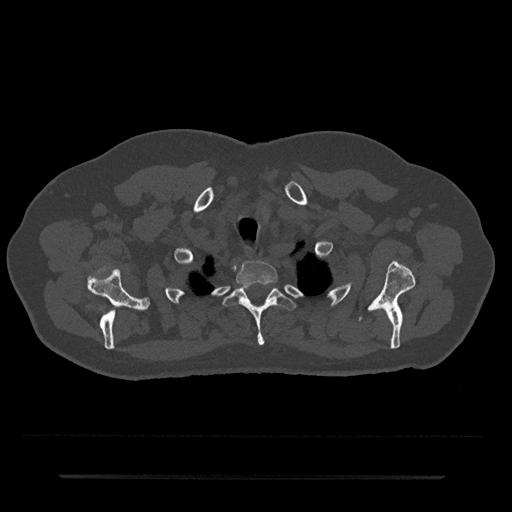
CT including the spine, one axial slice. Position 616 of 797 along the scan axis. Bone window (W 1800 / L 400 HU). 512 × 512 image matrix, field of view 437 × 437 mm. Patient: male, 69 years. Case-level facts recorded for this patient, not image findings: primary cancer: prostate.
Outlined on this slice (semi-automatic segmentation, software-assisted and operator-edited):
- T1 vertebra: bounding box <236,260,278,288> (left, top, right, bottom; pixels)
- T2 vertebra: <223,282,295,345>